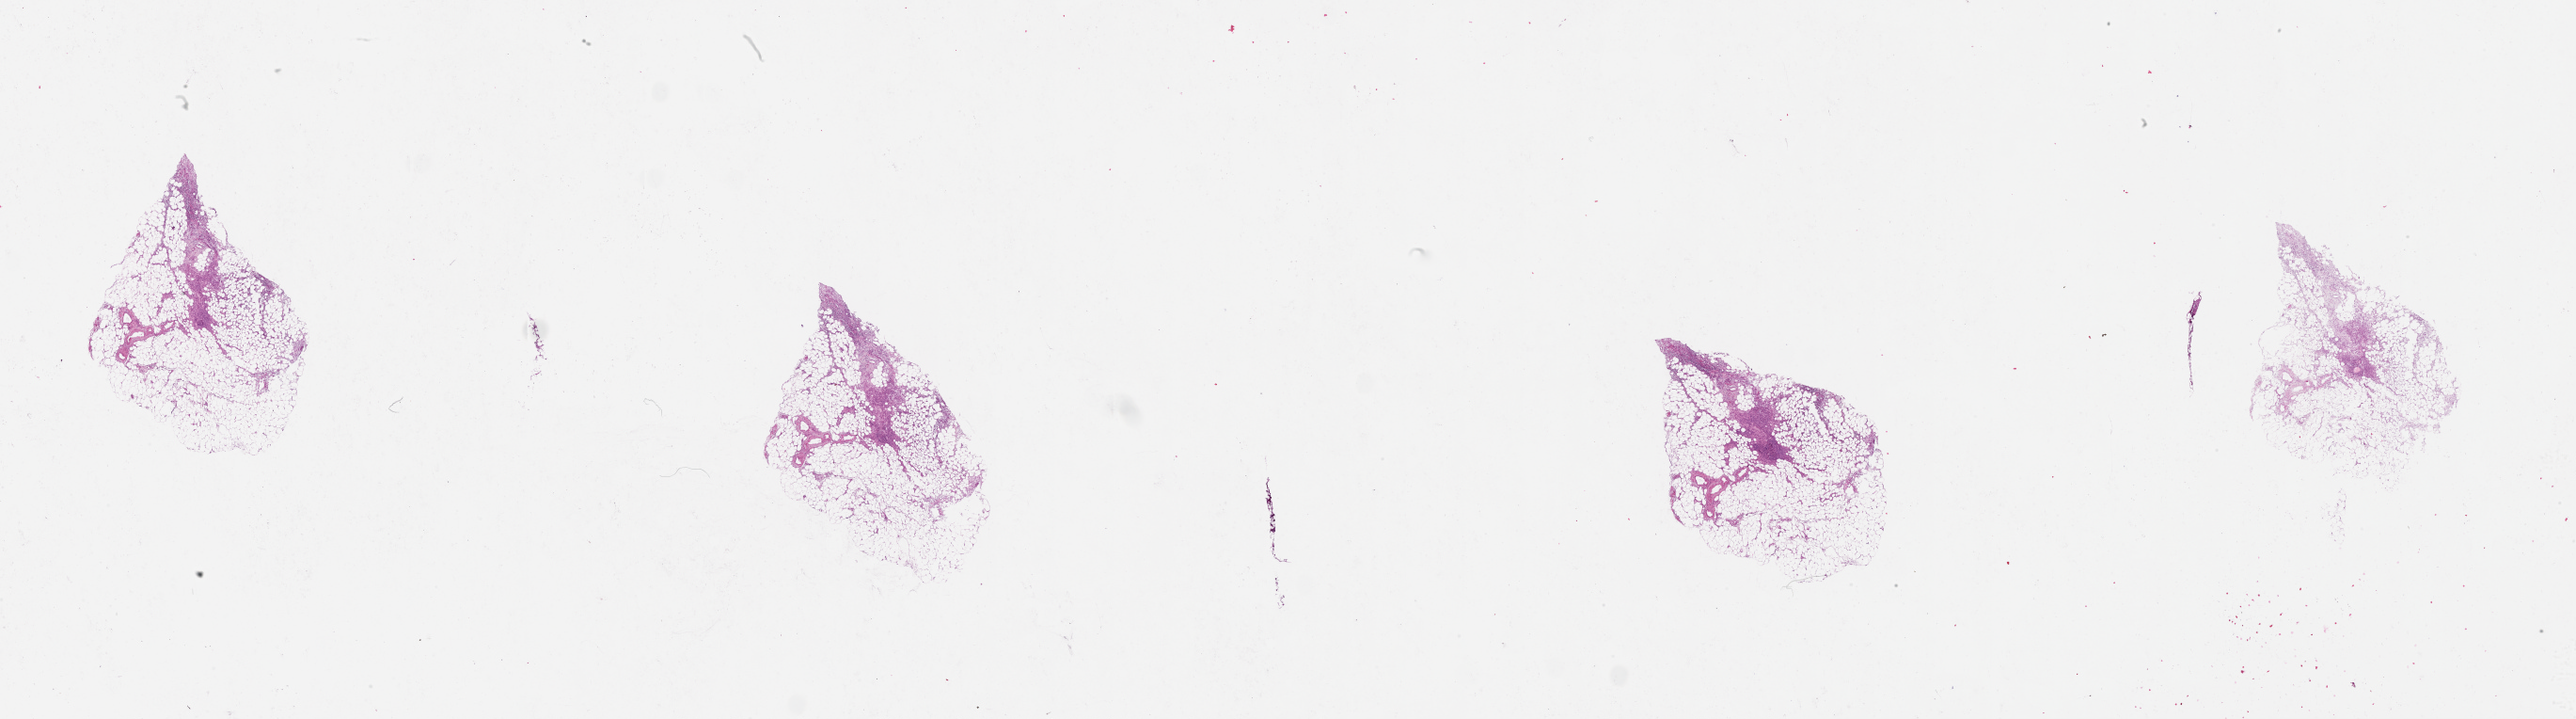
H&E-stained whole-slide image, whole scanned area (about 44.1 x 12.3 mm, acquisition: 20x scan) shown as a low-resolution overview, pancreas, normal (non-tumour) tissue. 80-year-old female patient.
* this section: normal (non-tumour) tissue from the same patient
* patient diagnosis: Infiltrating duct carcinoma, NOS